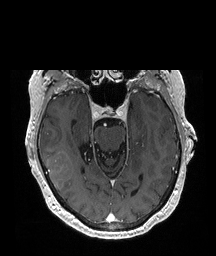
Brain MRI from a brain-tumour surgery series, one axial slice; position 133 of 208 along the scan axis; T1-weighted post-contrast; 1 mm slice thickness; 216 × 256 image matrix, field of view 216 × 256 mm. Case-level facts recorded for this patient, not image findings: histopathology: Glioblastoma; WHO grade: 4; IDH mutation: no.
Annotated regions visible in this slice (expert manual segmentation):
- tumour: bounding box (x1, y1, x2, y2) in pixels: (44, 152, 74, 191)